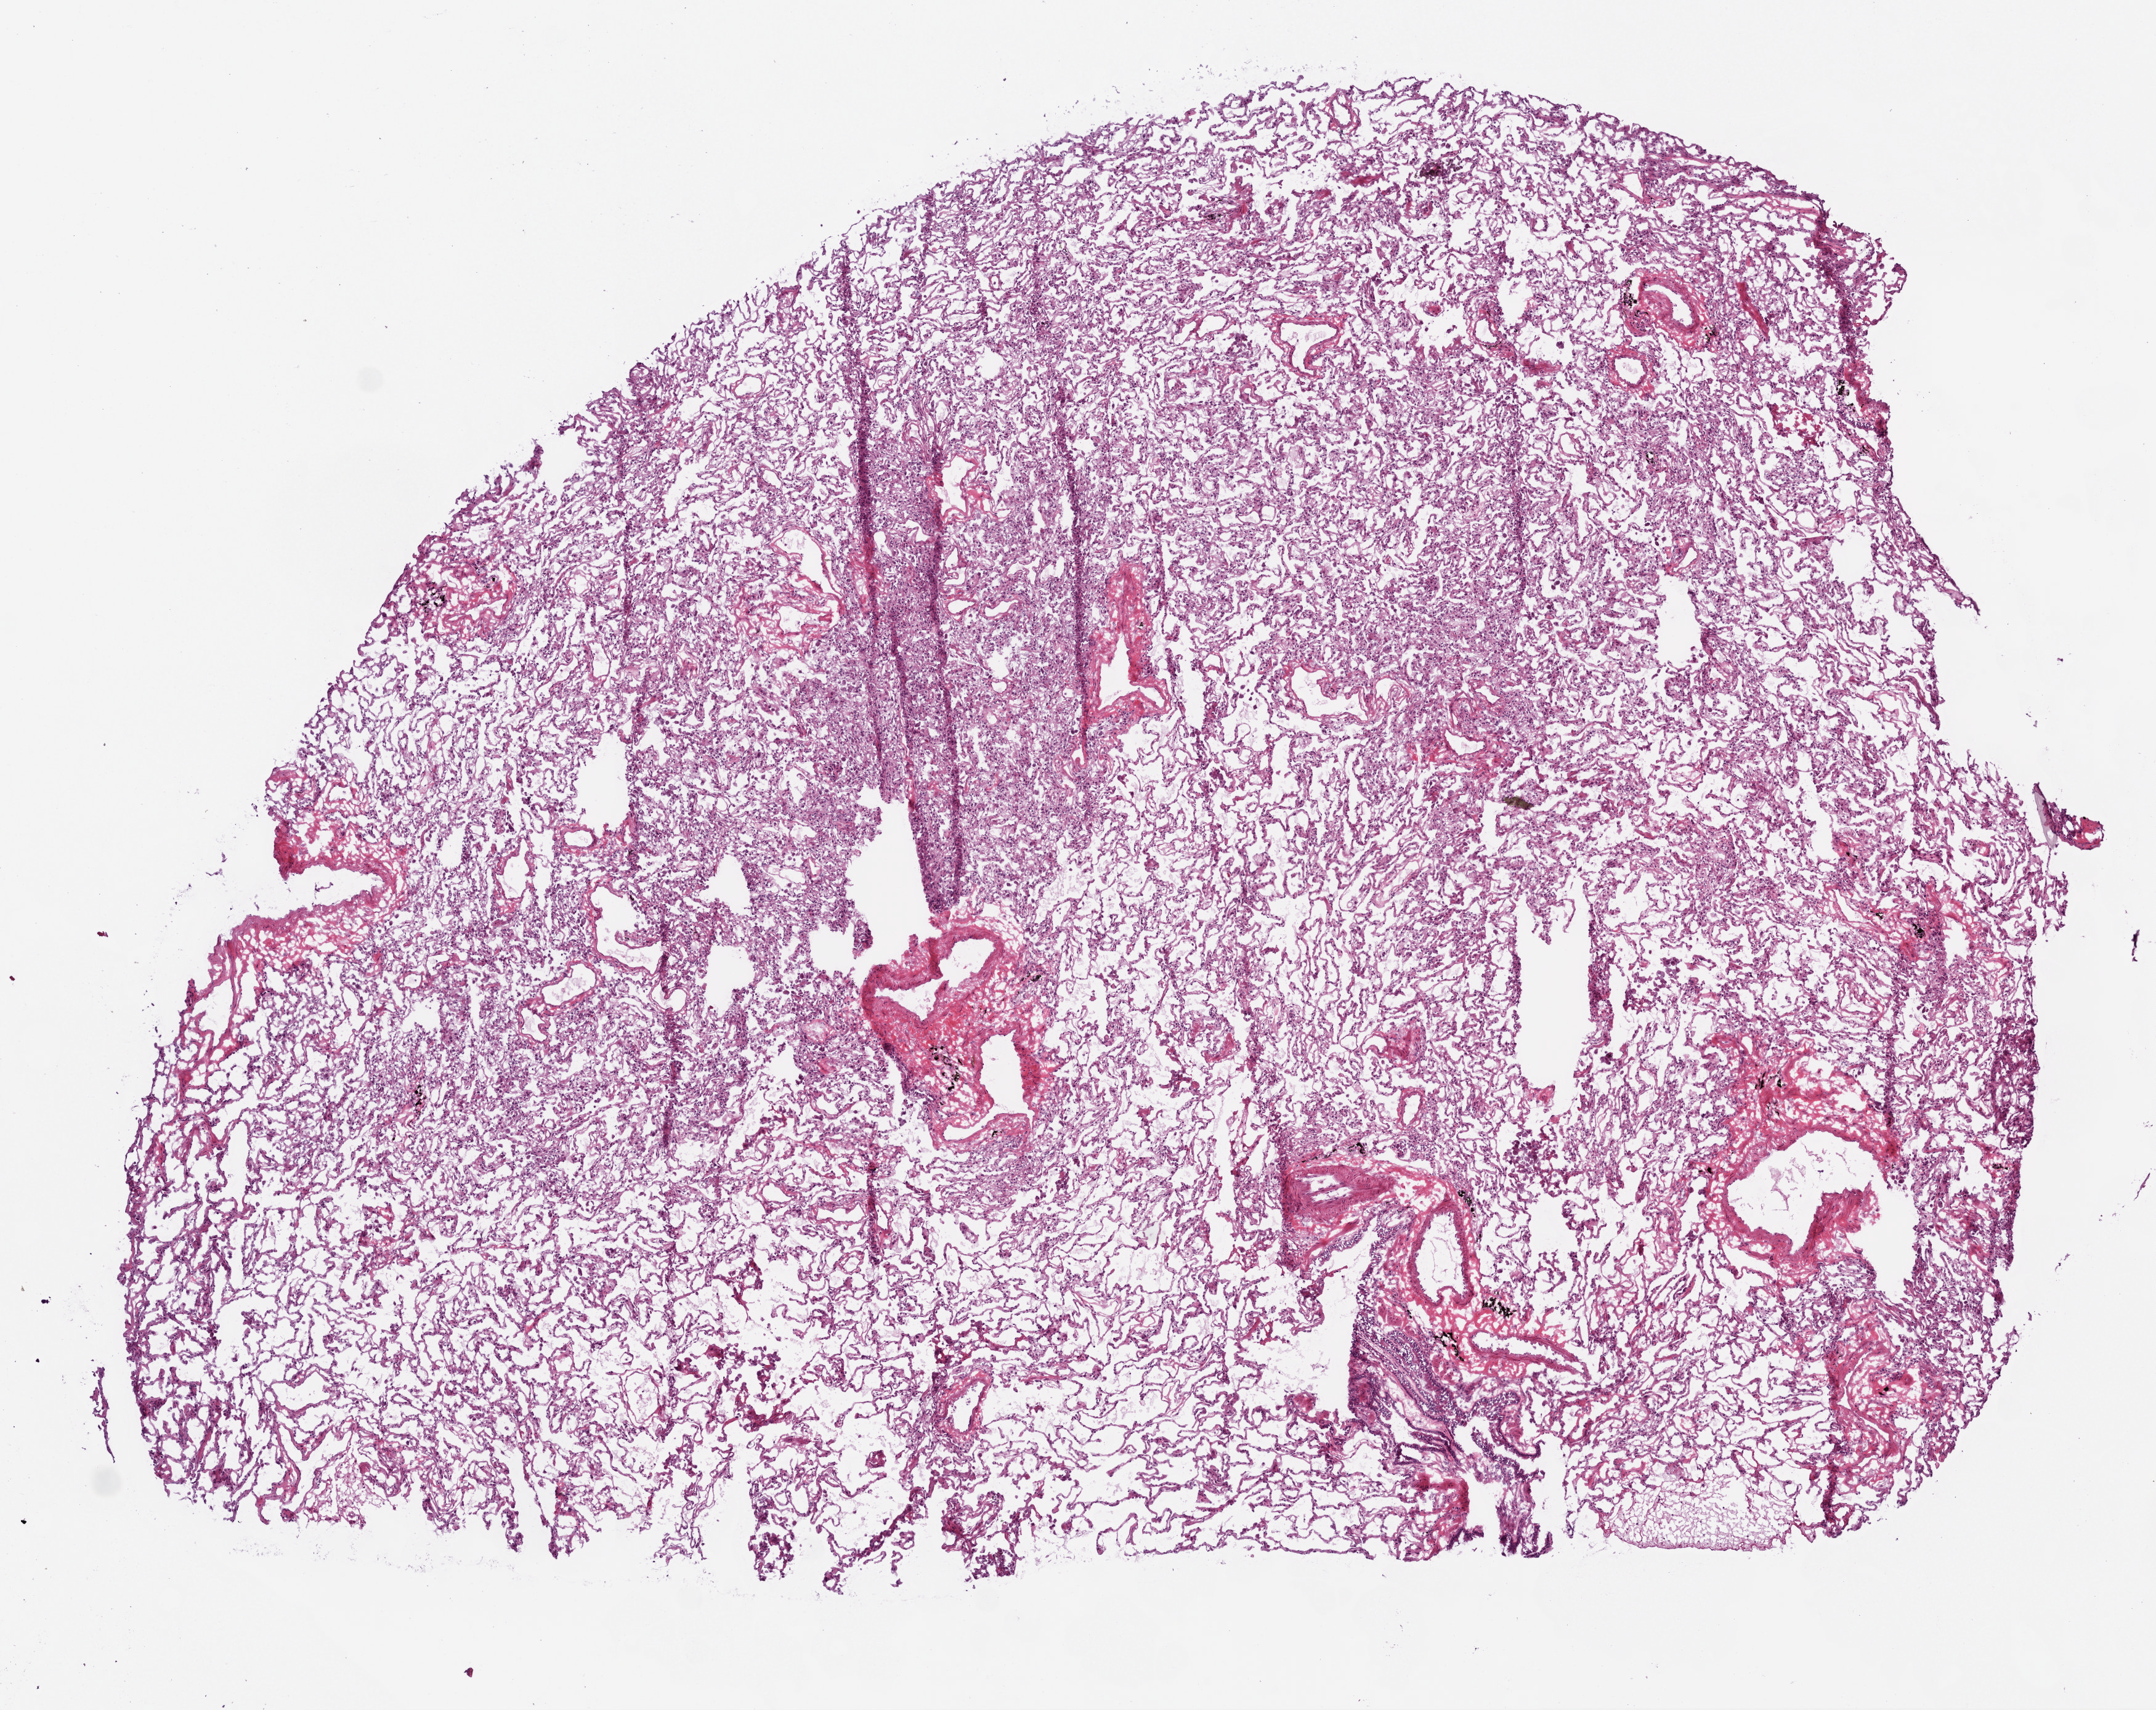
Digitized H&E tissue section (whole slide) — low-resolution overview of the scanned area, about 7.0 x 5.6 mm, frozen section from the bottom of the tissue portion, solid tissue normal (non-tumour tissue) sample from the lung. Male patient; age at initial diagnosis 64 years.
This section: solid tissue normal (non-tumour) sample from the same patient. Patient diagnosis: Squamous cell carcinoma, NOS.